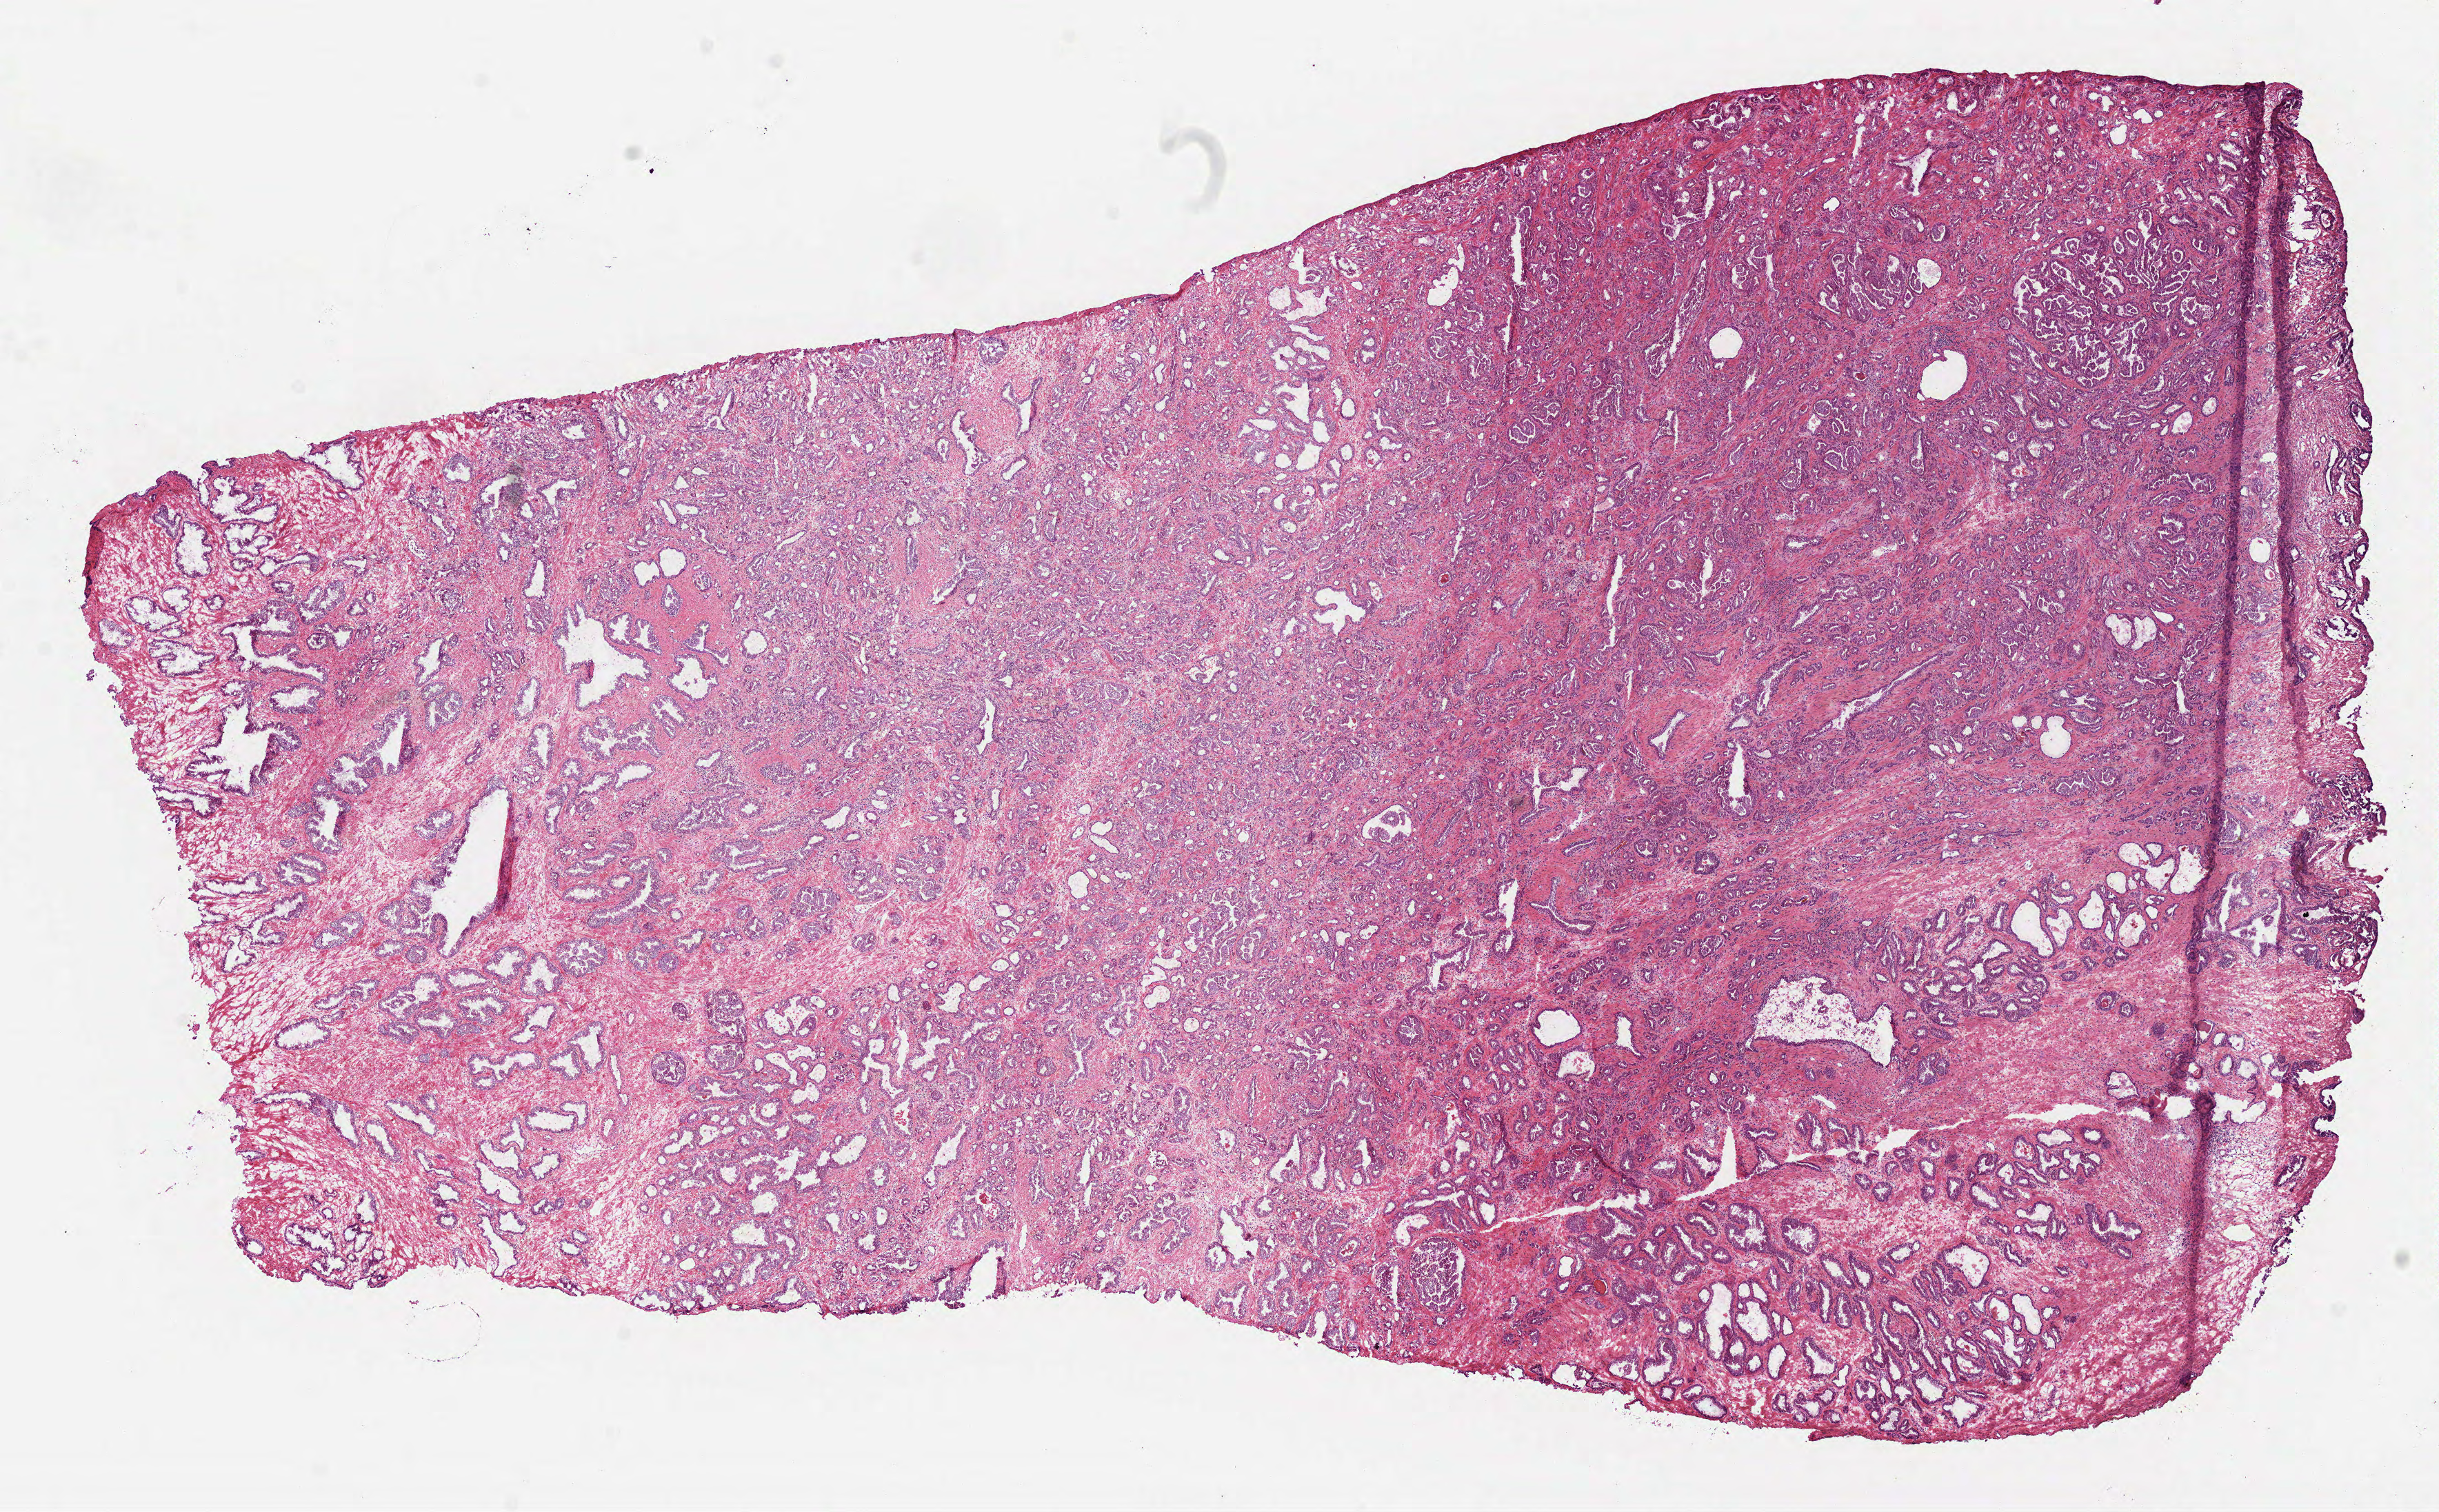
Digitized H&E-stained tissue section (whole slide), whole scanned area (about 14.3 x 8.8 mm, from a 40x scan) shown as a low-resolution overview, frozen section from the top of the tissue portion, prostate, primary tumour sample. Patient: male, age at initial diagnosis 52 years. Gleason score: 7 (4+3). Slide review estimates, as recorded: tumour cells 60%, tumour nuclei 60%, normal cells 25%, stromal cells 15%, necrosis 0%.
Lymph nodes positive (case pathology): 0 of 4 examined. Histologic diagnosis: Acinar cell carcinoma (prostate gland).